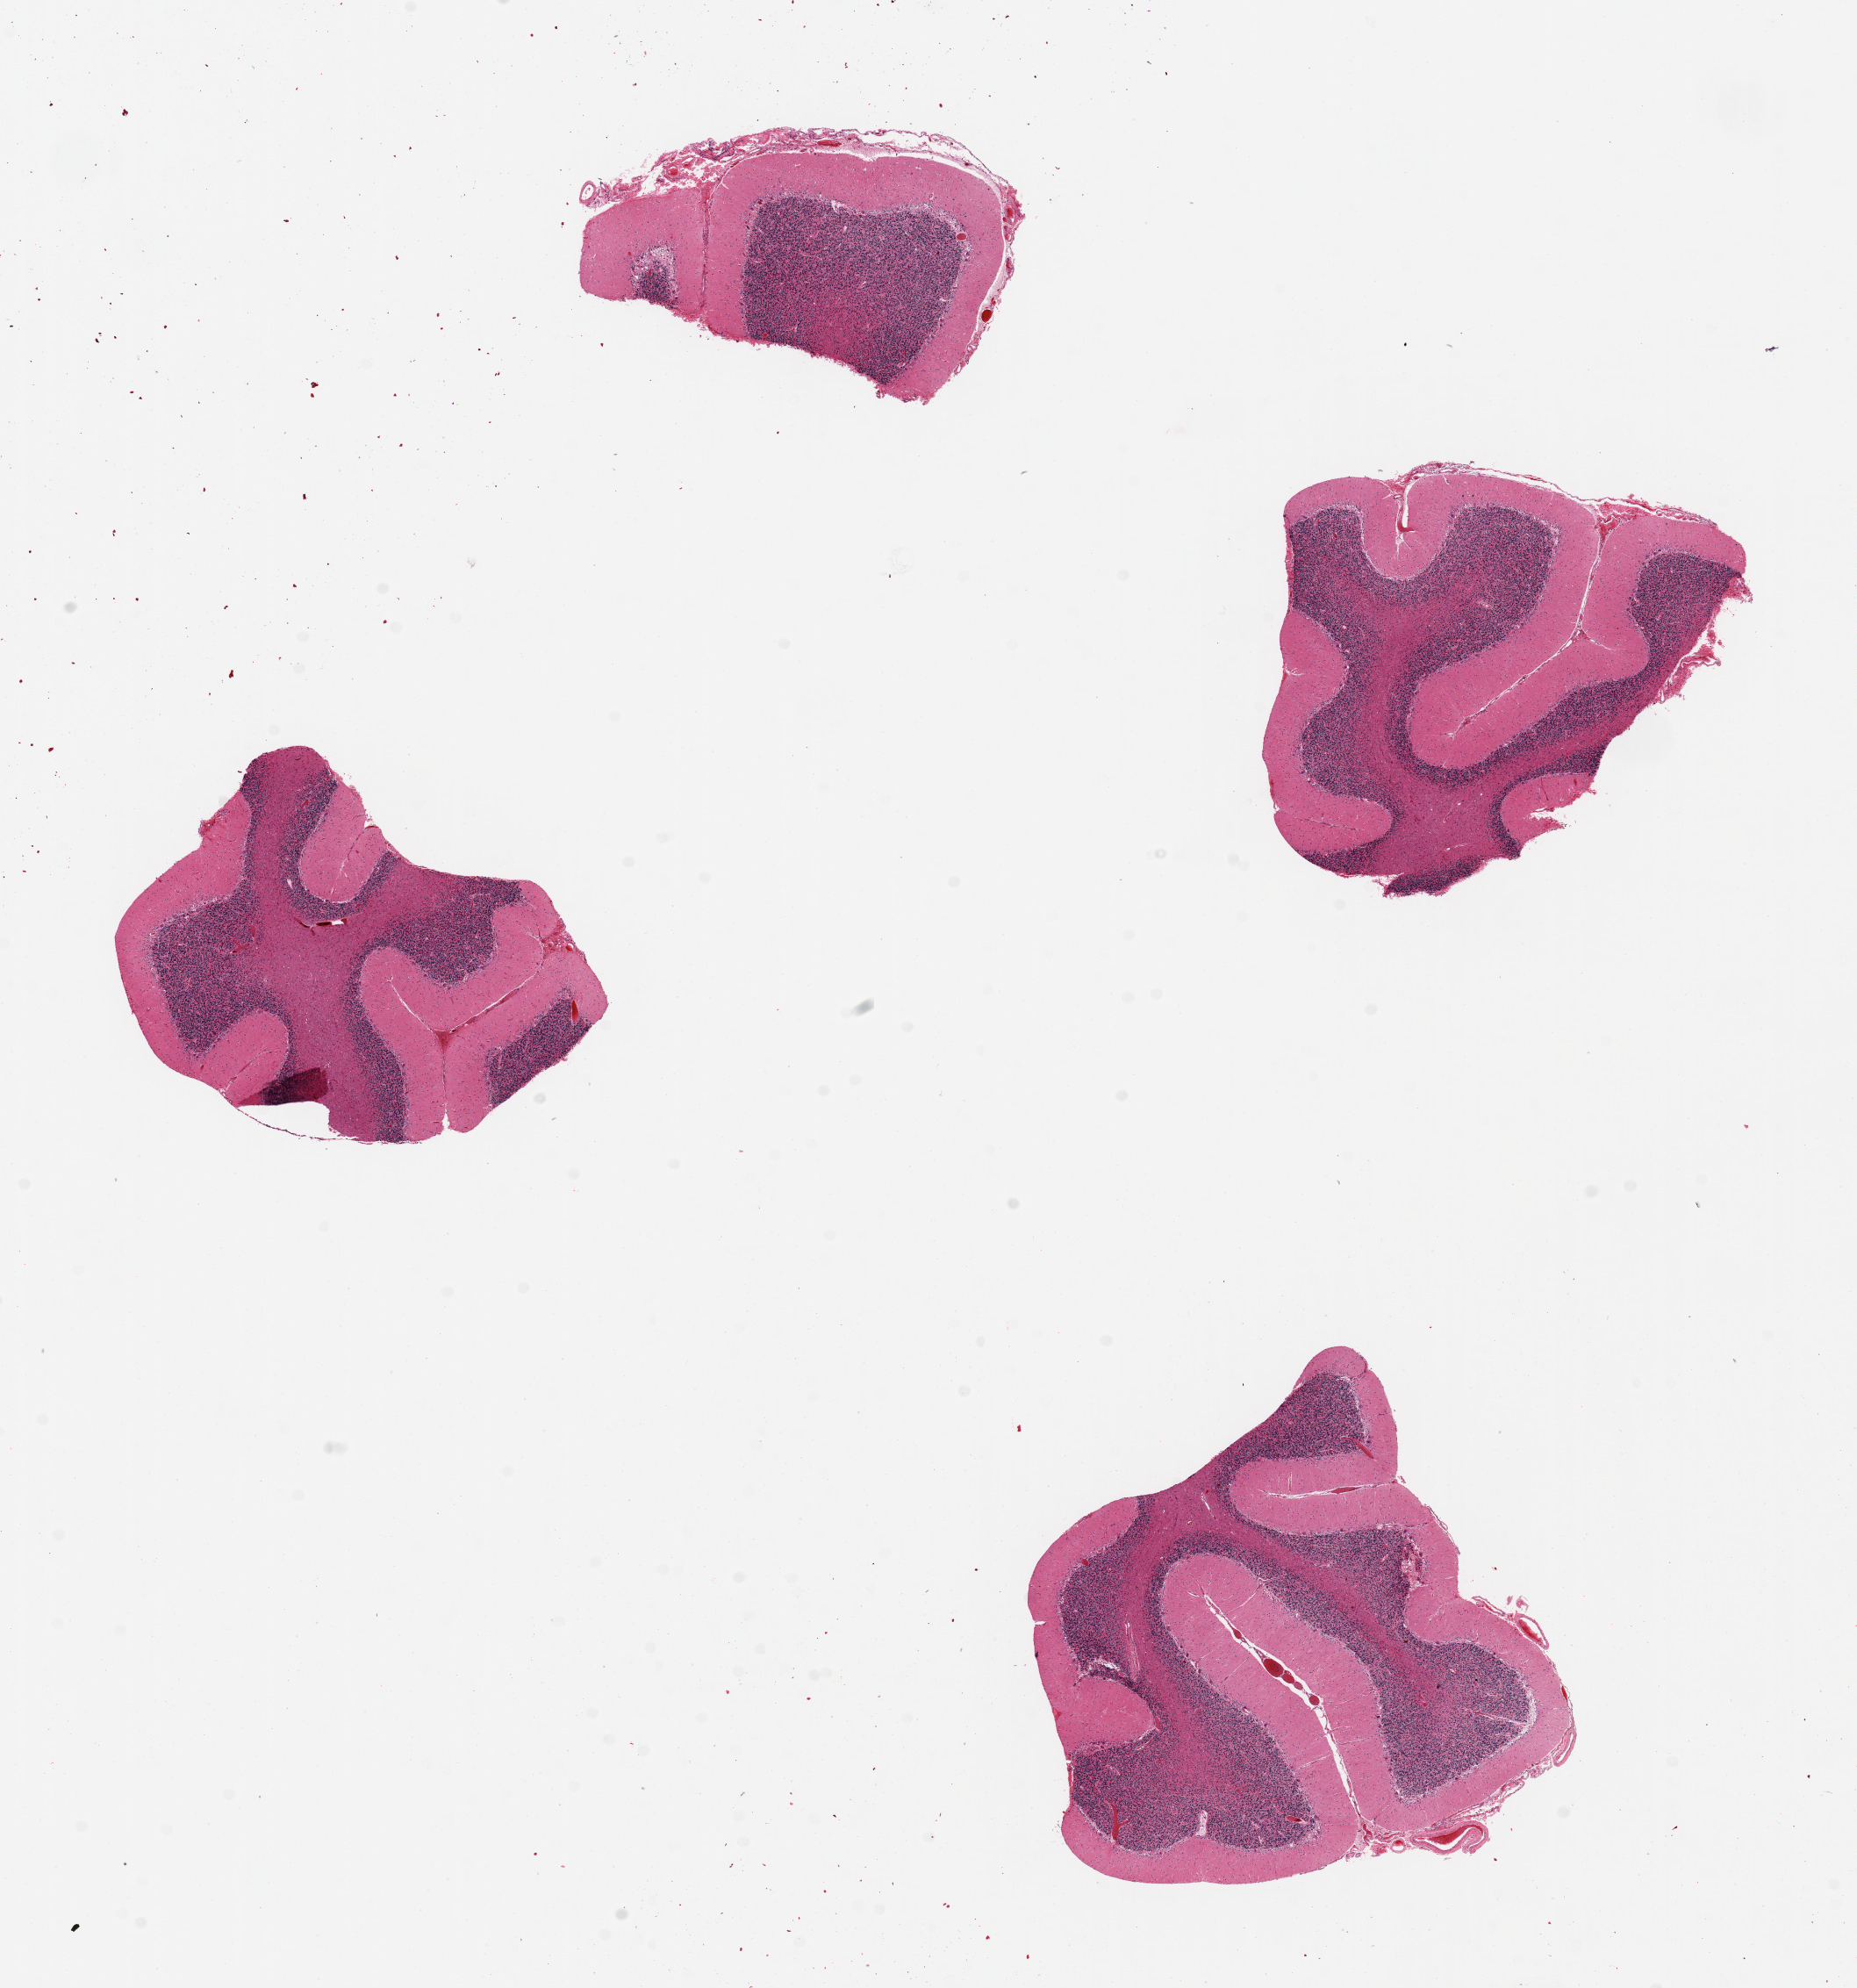
Digitized H&E-stained section, brightfield, low-resolution overview of the scanned area, about 16.7 x 17.9 mm, PAXgene-fixed paraffin-embedded (PFPE) section, sampled site (target tissue): cerebellum, tissue donor sample. Donor: female.
Reviewer comment on this tissue sample: 4 pieces ~4x4mm. Reasonably well preserved, Purkinje cells show signs of antemortem ischemia (nuclear smudging).